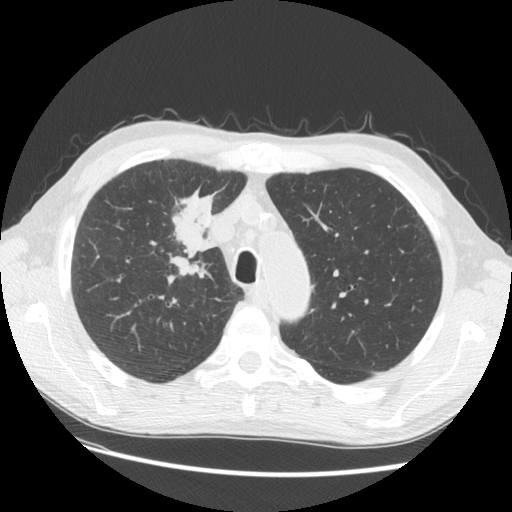
Low-dose screening chest CT, one axial slice; position 102 of 133 along the scan axis; lung window (W 1500 / L -600 HU); 512 × 512 image matrix, field of view 360 × 360 mm.
Structures marked on this image (outlined manually by an expert reader):
- lesion 1 (tumor, hilum of right lung): bounding box (x1, y1, x2, y2) in pixels: (168, 185, 217, 276)